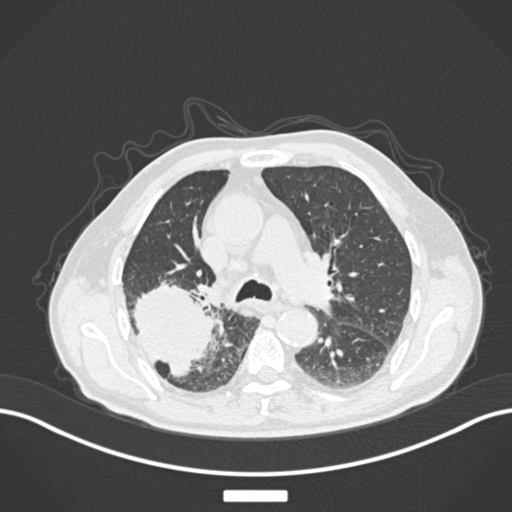
Chest CT, one axial slice; position 113 of 201 along the scan axis; 120 kVp; lung window (W 1500 / L -600 HU); 512 × 512 image matrix, field of view 400 × 400 mm. Male patient, age 72 years. From the clinical record (not read from this slice): clinical TNM (as recorded): T3 N2 M0.
Structures marked on this image (rectangle marked by the reading radiologist):
- lung tumour (recorded histology: adenocarcinoma): box from (x=129, y=278) to (x=216, y=379) px